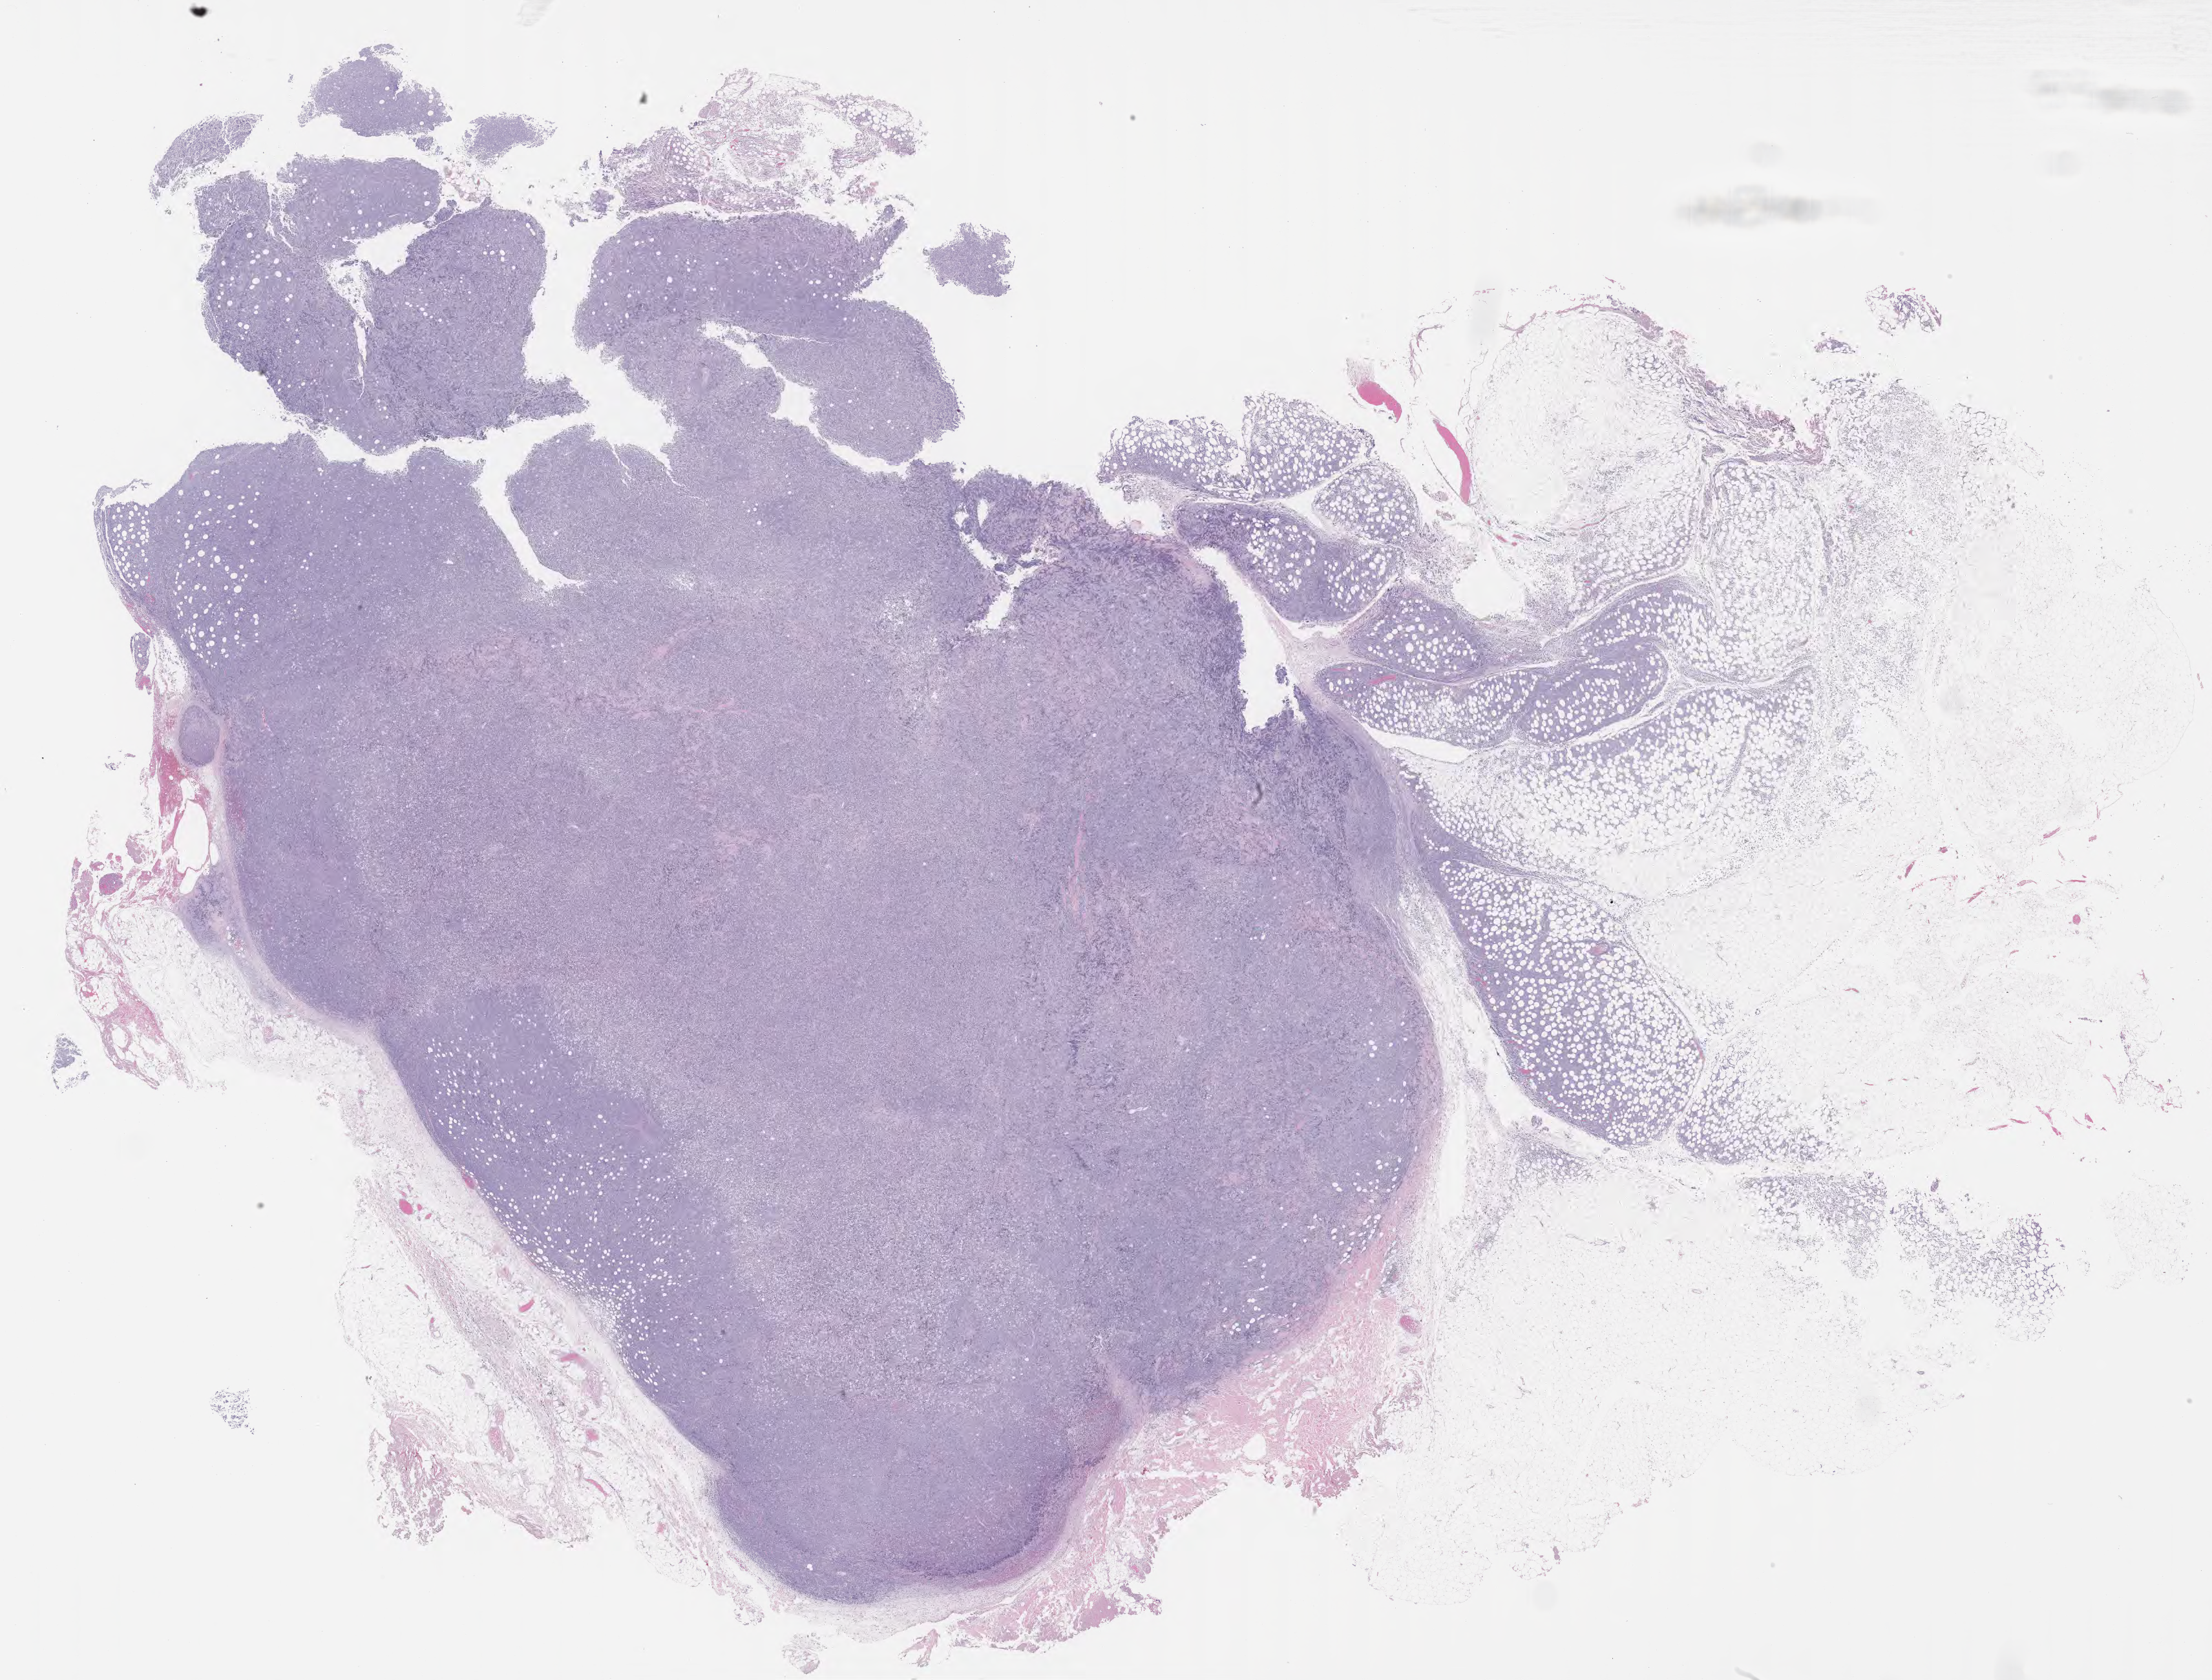
Digitized H&E-stained section — low-resolution overview of the scanned area, about 27.7 x 21.0 mm, specimen: tumor tissue. Patient male; aged 71.
Diagnosis: Burkitt lymphoma, NOS.